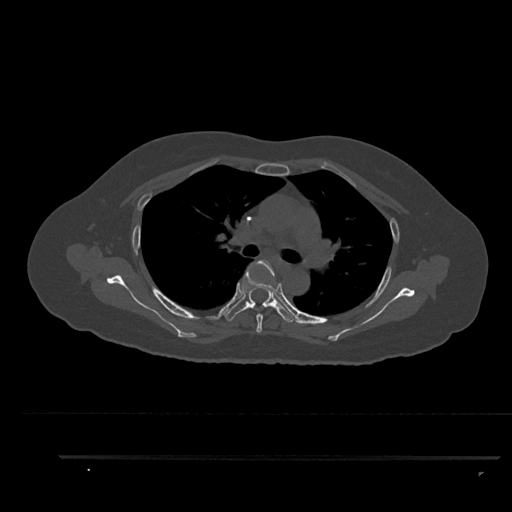
CT including the spine, one axial slice; slice 617 of 797 in the series (ordered by position); reconstruction kernel Br40s/3; bone window (W 1800 / L 400 HU); 0.5 mm slice thickness; 512 × 512 image matrix, field of view 408 × 408 mm. Female patient, age 44 years. From the clinical record (not read from this slice): primary cancer: renal; vertebrae with lytic lesions (as recorded): L1.
Outlined on this slice (semi-automatically segmented with operator editing):
- T4 vertebra: bounding box [x1, y1, x2, y2] px = [253, 260, 275, 333]
- T5 vertebra: [224, 274, 296, 322]